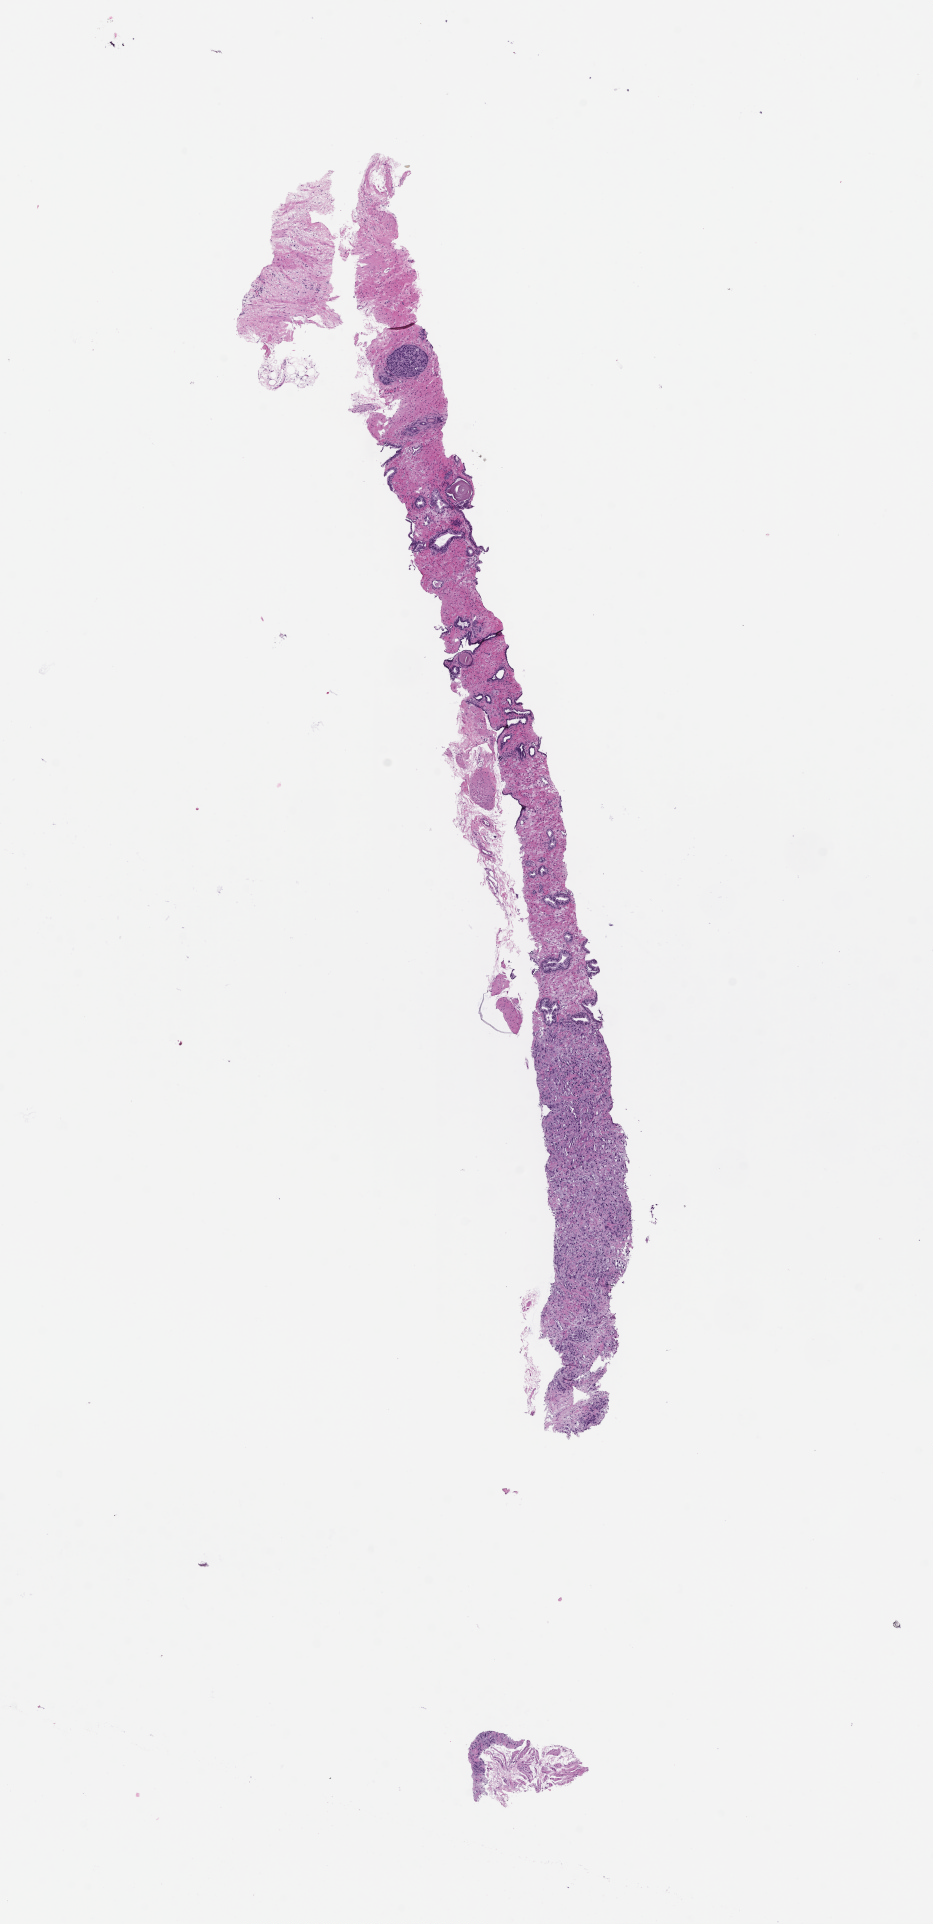
Whole-slide image, haematoxylin and eosin stain, whole scanned area (about 7.5 x 15.5 mm) shown as a low-resolution overview; FFPE section; site: prostate; specimen time point: archival tissue. Male patient.
• this section: primary tumour tissue
• diagnosis: Prostate Carcinoma